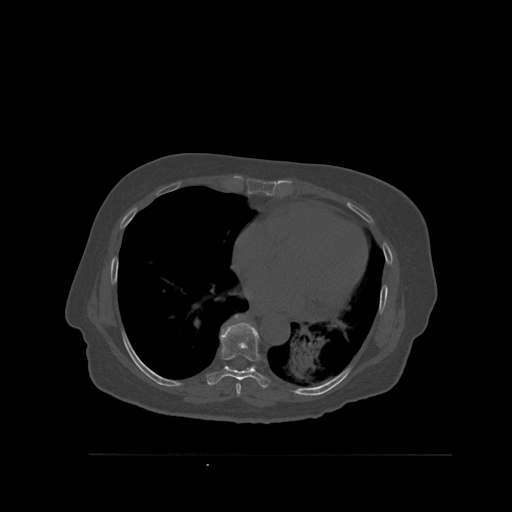
CT including the spine, one axial slice; slice 350 of 527 in the series (ordered by position); bone window (W 1800 / L 400 HU); 512 × 512 image matrix, field of view 470 × 470 mm. Female patient, age 73 years. Case-level facts recorded for this patient, not image findings: primary cancer: breast; vertebrae with lytic lesions (as recorded): L2.
Structures marked on this image (semi-automatically segmented with operator editing):
- T7 vertebra: bounding box (x1, y1, x2, y2) in pixels: (236, 383, 241, 396)
- T8 vertebra: (207, 323, 270, 388)
- T9 vertebra: (225, 314, 255, 367)